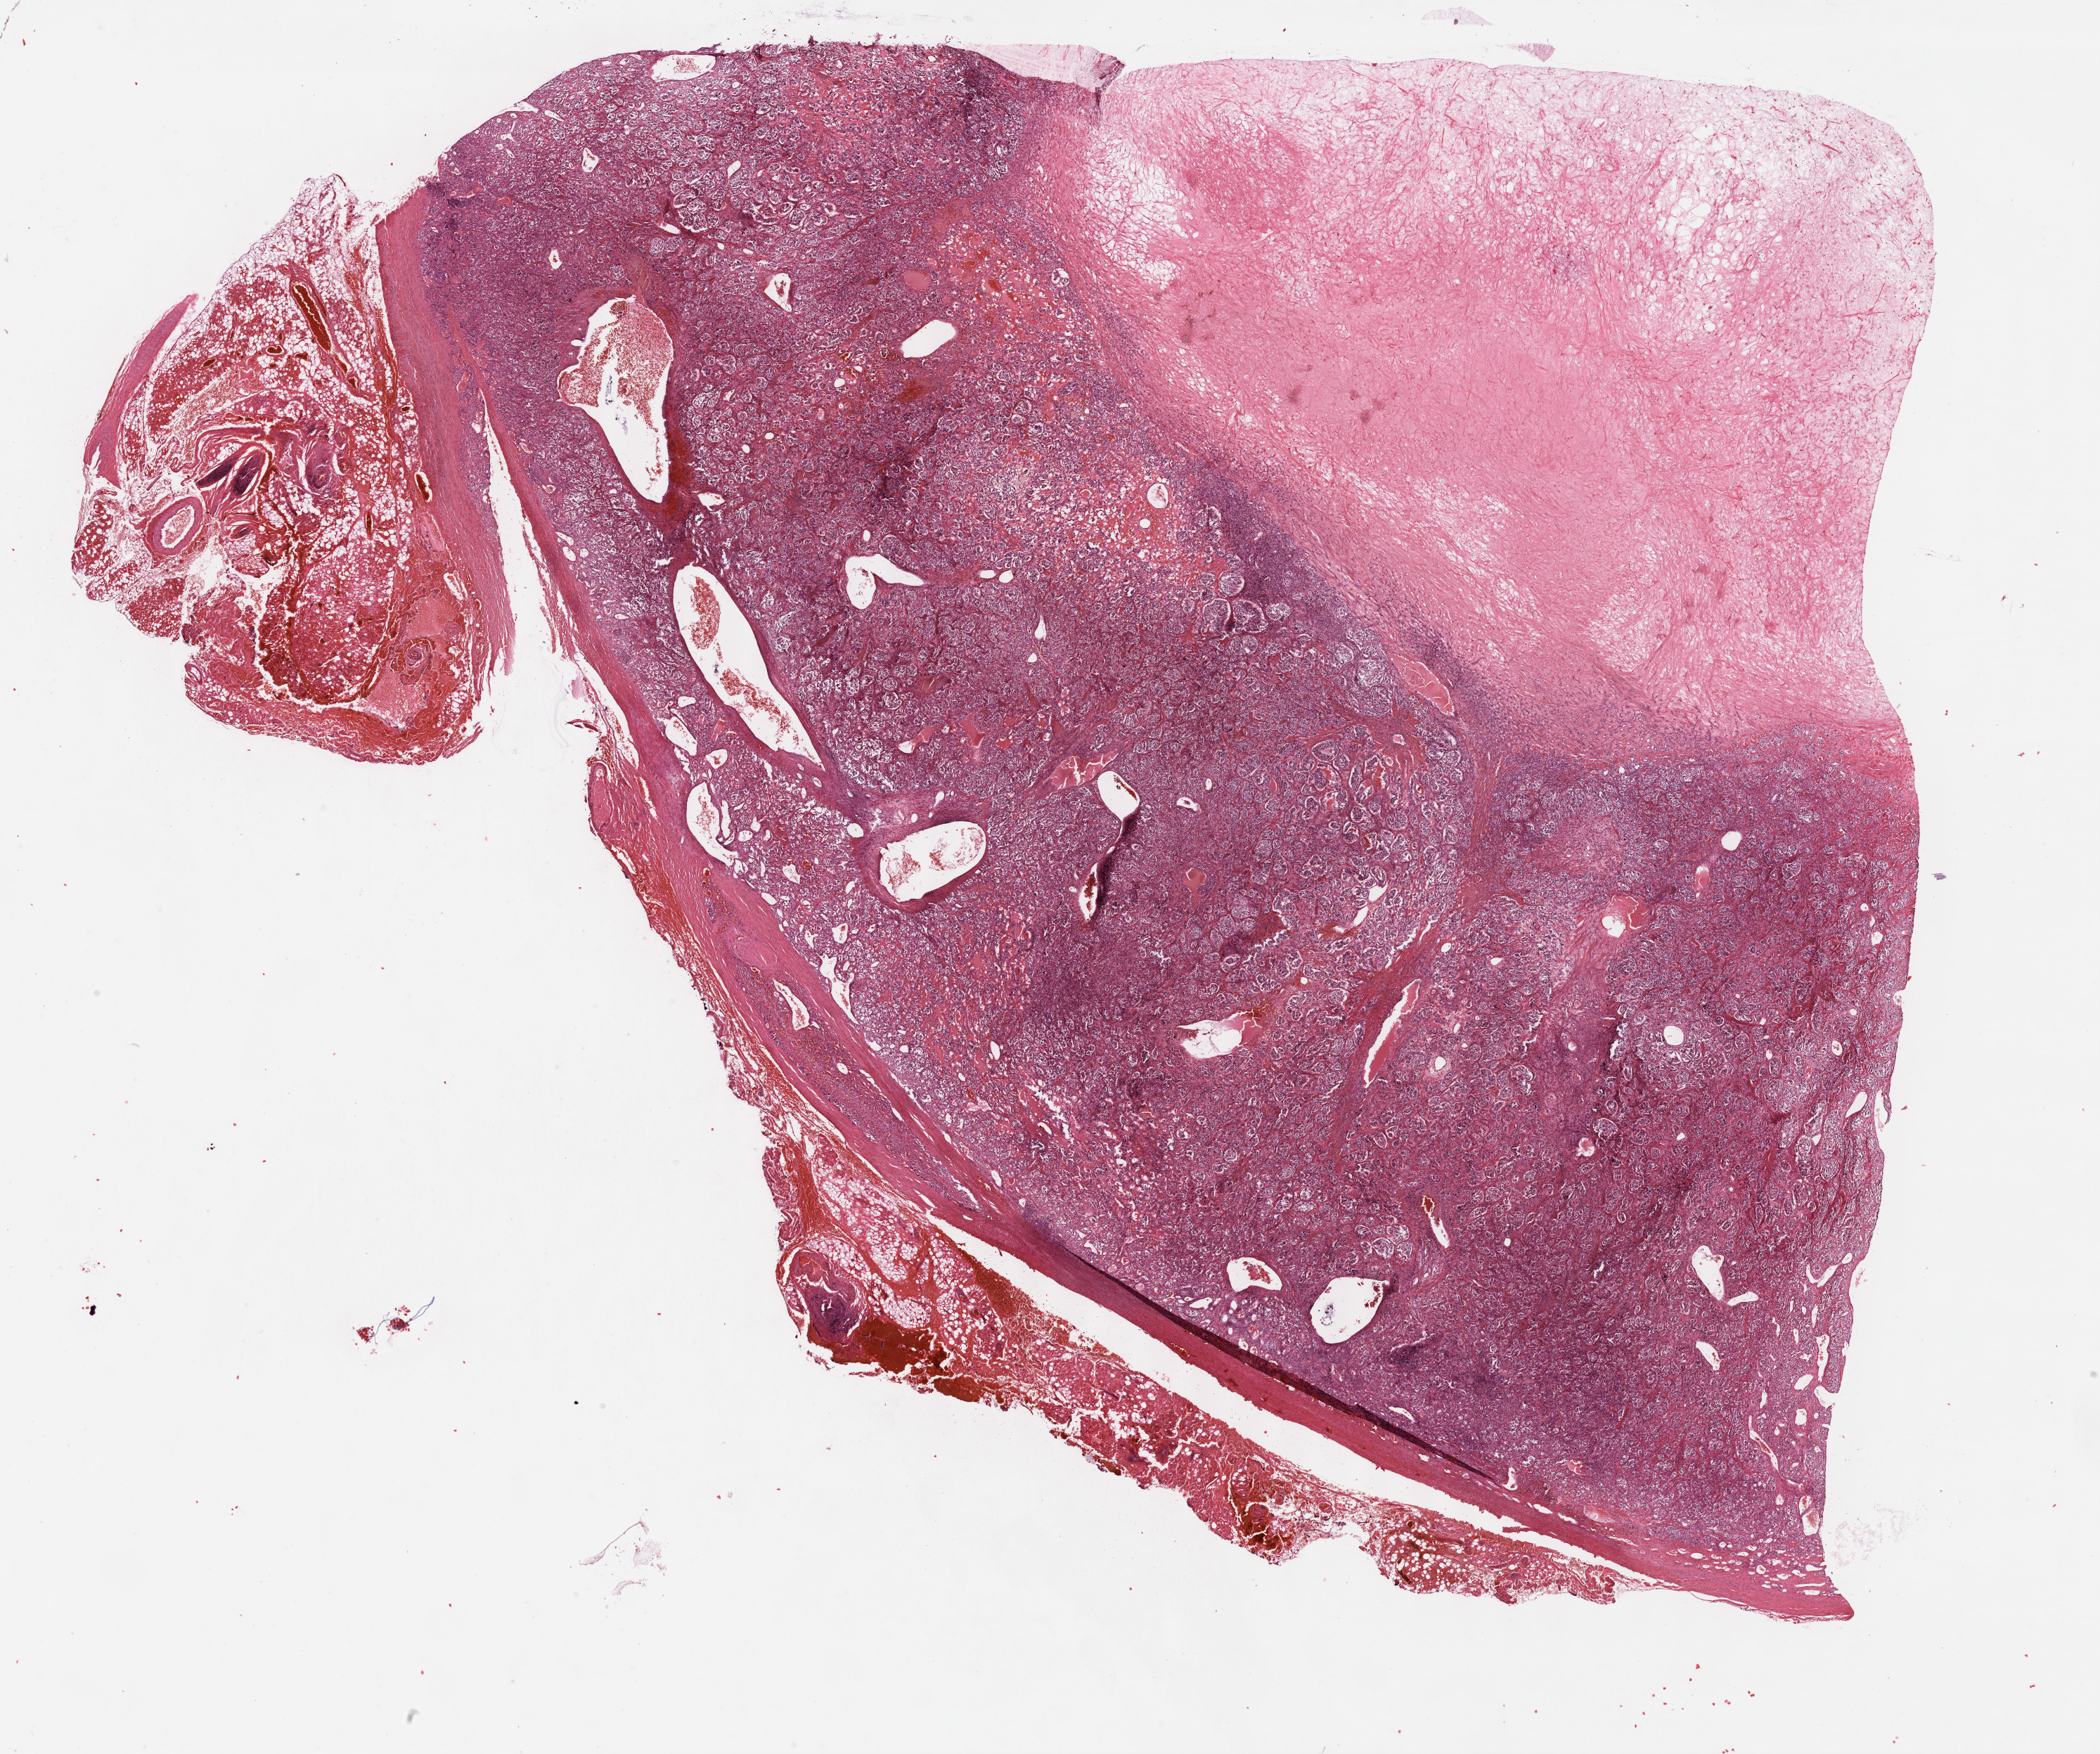
Digitized H&E-stained tissue section (whole slide) — a low-resolution overview of the entire scanned area, about 24.2 x 20.2 mm. Formalin-fixed paraffin-embedded (FFPE) diagnostic section. Adrenal gland, primary tumour sample. Male, age 23 years at initial diagnosis.
- laterality: right
- histologic diagnosis: Clear cell carcinoma (kidney, NOS)